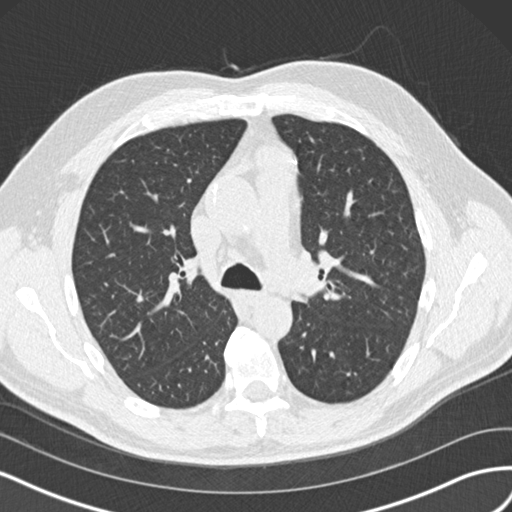
Chest CT (low-dose screening protocol), one axial image; baseline annual screen; lung window (W 1500 / L -600 HU); 2 mm slice thickness; standard (soft-tissue) reconstruction kernel (B30f); slice 56 of 160 in the series. Male, age 65 years at enrolment. Former smoker at enrolment.
Lesion marked by an expert reader, bounding box (x1, y1, x2, y2) in pixels: (308, 241, 353, 297). The screening reader recorded 4 non-calcified nodules or masses ≥4 mm on this exam (left upper lobe, left upper lobe, right upper lobe, right middle lobe); which of them this box marks is not recorded. Later outcome: lung cancer diagnosed 945 days after this screen (after the third annual screen) — acinar cell carcinoma, left upper lobe, stage IA (AJCC 6th edition), 25 mm at pathology.